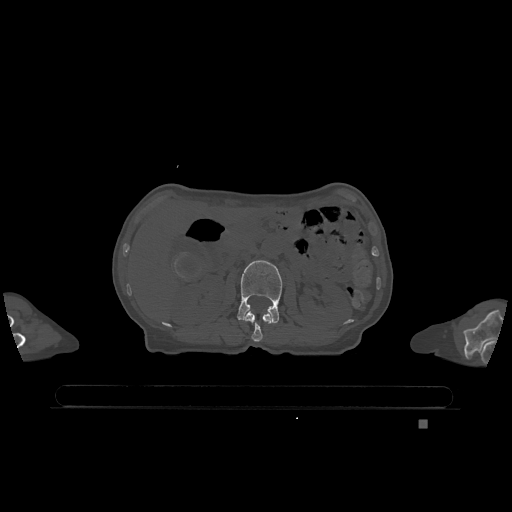
CT including the spine, one axial slice. Bone window (W 1800 / L 400 HU). 0.5 mm slice thickness. 512 × 512 image matrix. Patient: female, 74 years. Case-level facts recorded for this patient, not image findings: primary cancer: lung.
Outlined on this slice (semi-automatic segmentation, software-assisted and operator-edited):
- L1 vertebra: bounding box <244,310,272,342> (left, top, right, bottom; pixels)
- L2 vertebra: <237,260,283,323>